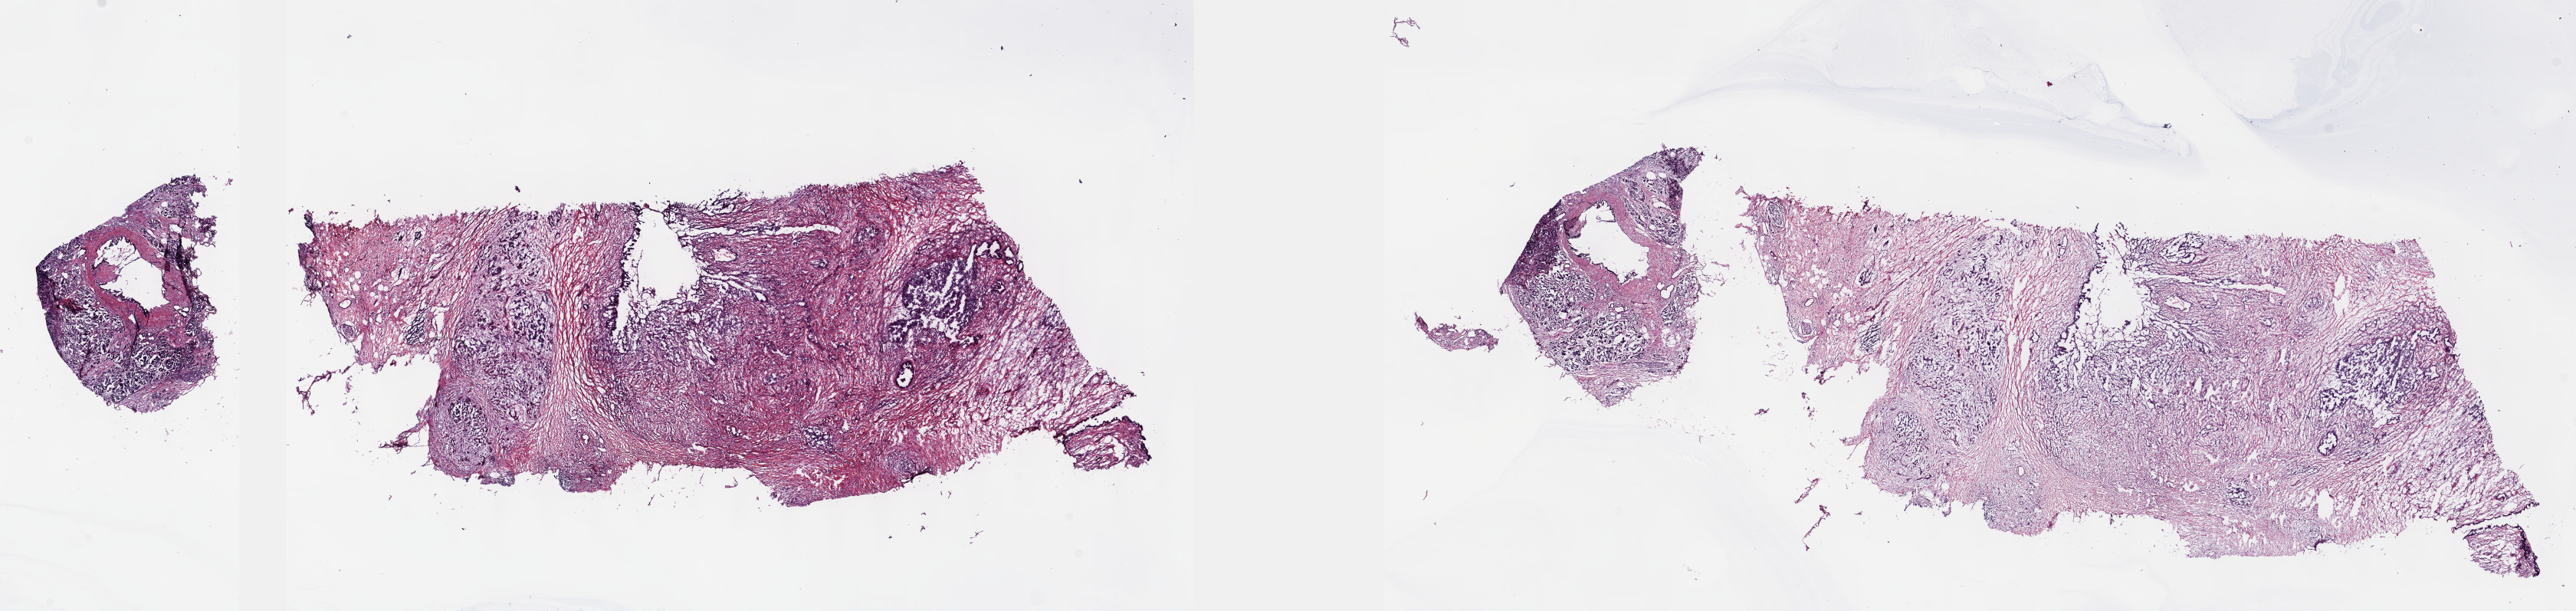
Digitized H&E-stained tissue section (whole slide), low-resolution overview of the scanned area, about 27.2 x 6.4 mm (acquisition: 40x scan), frozen section, primary tumour sample from the bile duct. Male patient. Histologic grade: G3 (poorly differentiated). Composition of this section per pathologist review: tumour cells 40%, tumour nuclei 80%, normal cells 0%, stromal cells 56%, necrosis 4%. Infiltration values recorded for this section: lymphocyte infiltration 13%, monocyte infiltration 1%, neutrophil infiltration 1%.
AJCC pathologic stage: IIB (7th edition). Pathologic diagnosis: Cholangiocarcinoma (extrahepatic bile duct).